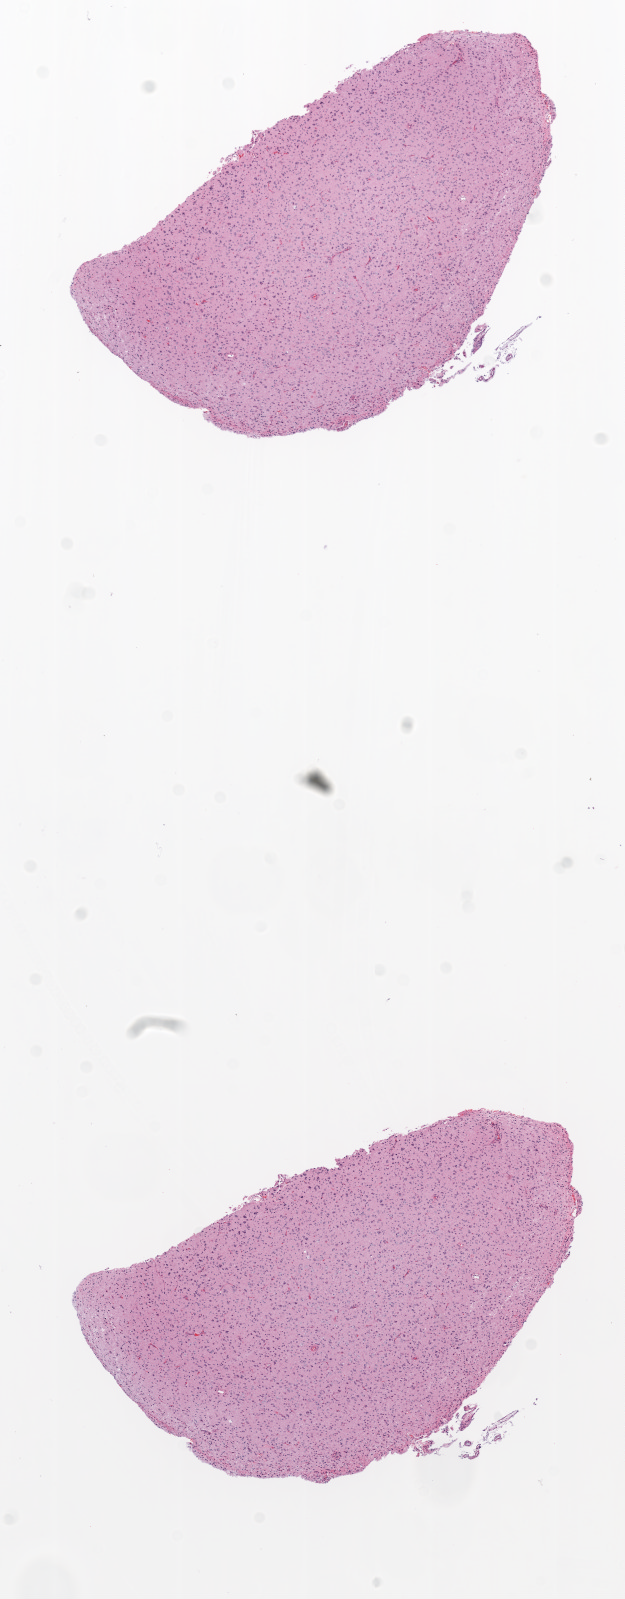
Whole-slide histology image, Hematoxylin and eosin (H&E) stained — low-resolution overview of the scanned area, about 5.0 x 12.8 mm (acquisition: 20x scan), FFPE section, primary tumour sample from the brain. Female, age 73 years at initial diagnosis.
Histologic diagnosis: Glioblastoma.